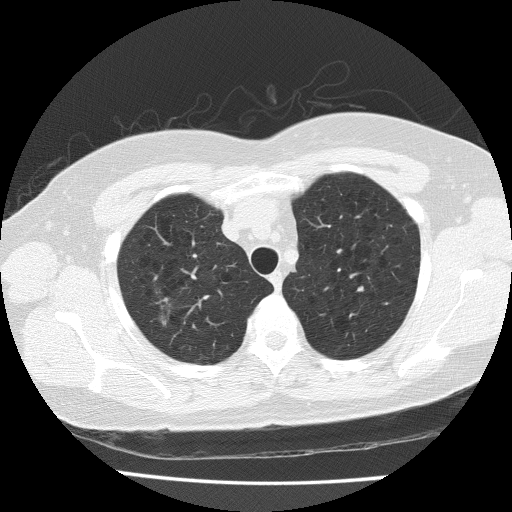
Axial slice from a low-dose chest CT screening exam; first (baseline) screen; lung window (W 1500 / L -600 HU); lung (sharp) reconstruction kernel (FC51); slice 33 of 175 in the series. Female participant, aged 57 years at enrolment. Former smoker at enrolment.
Expert reader's lesion annotation, box from (x=132, y=282) to (x=181, y=333) px. Reader record for this screening exam (exam-level; its link to the box is not recorded): non-calcified nodule or mass ≥4 mm, right upper lobe, 8 × 7 mm, spiculated (stellate) margins, soft tissue attenuation.